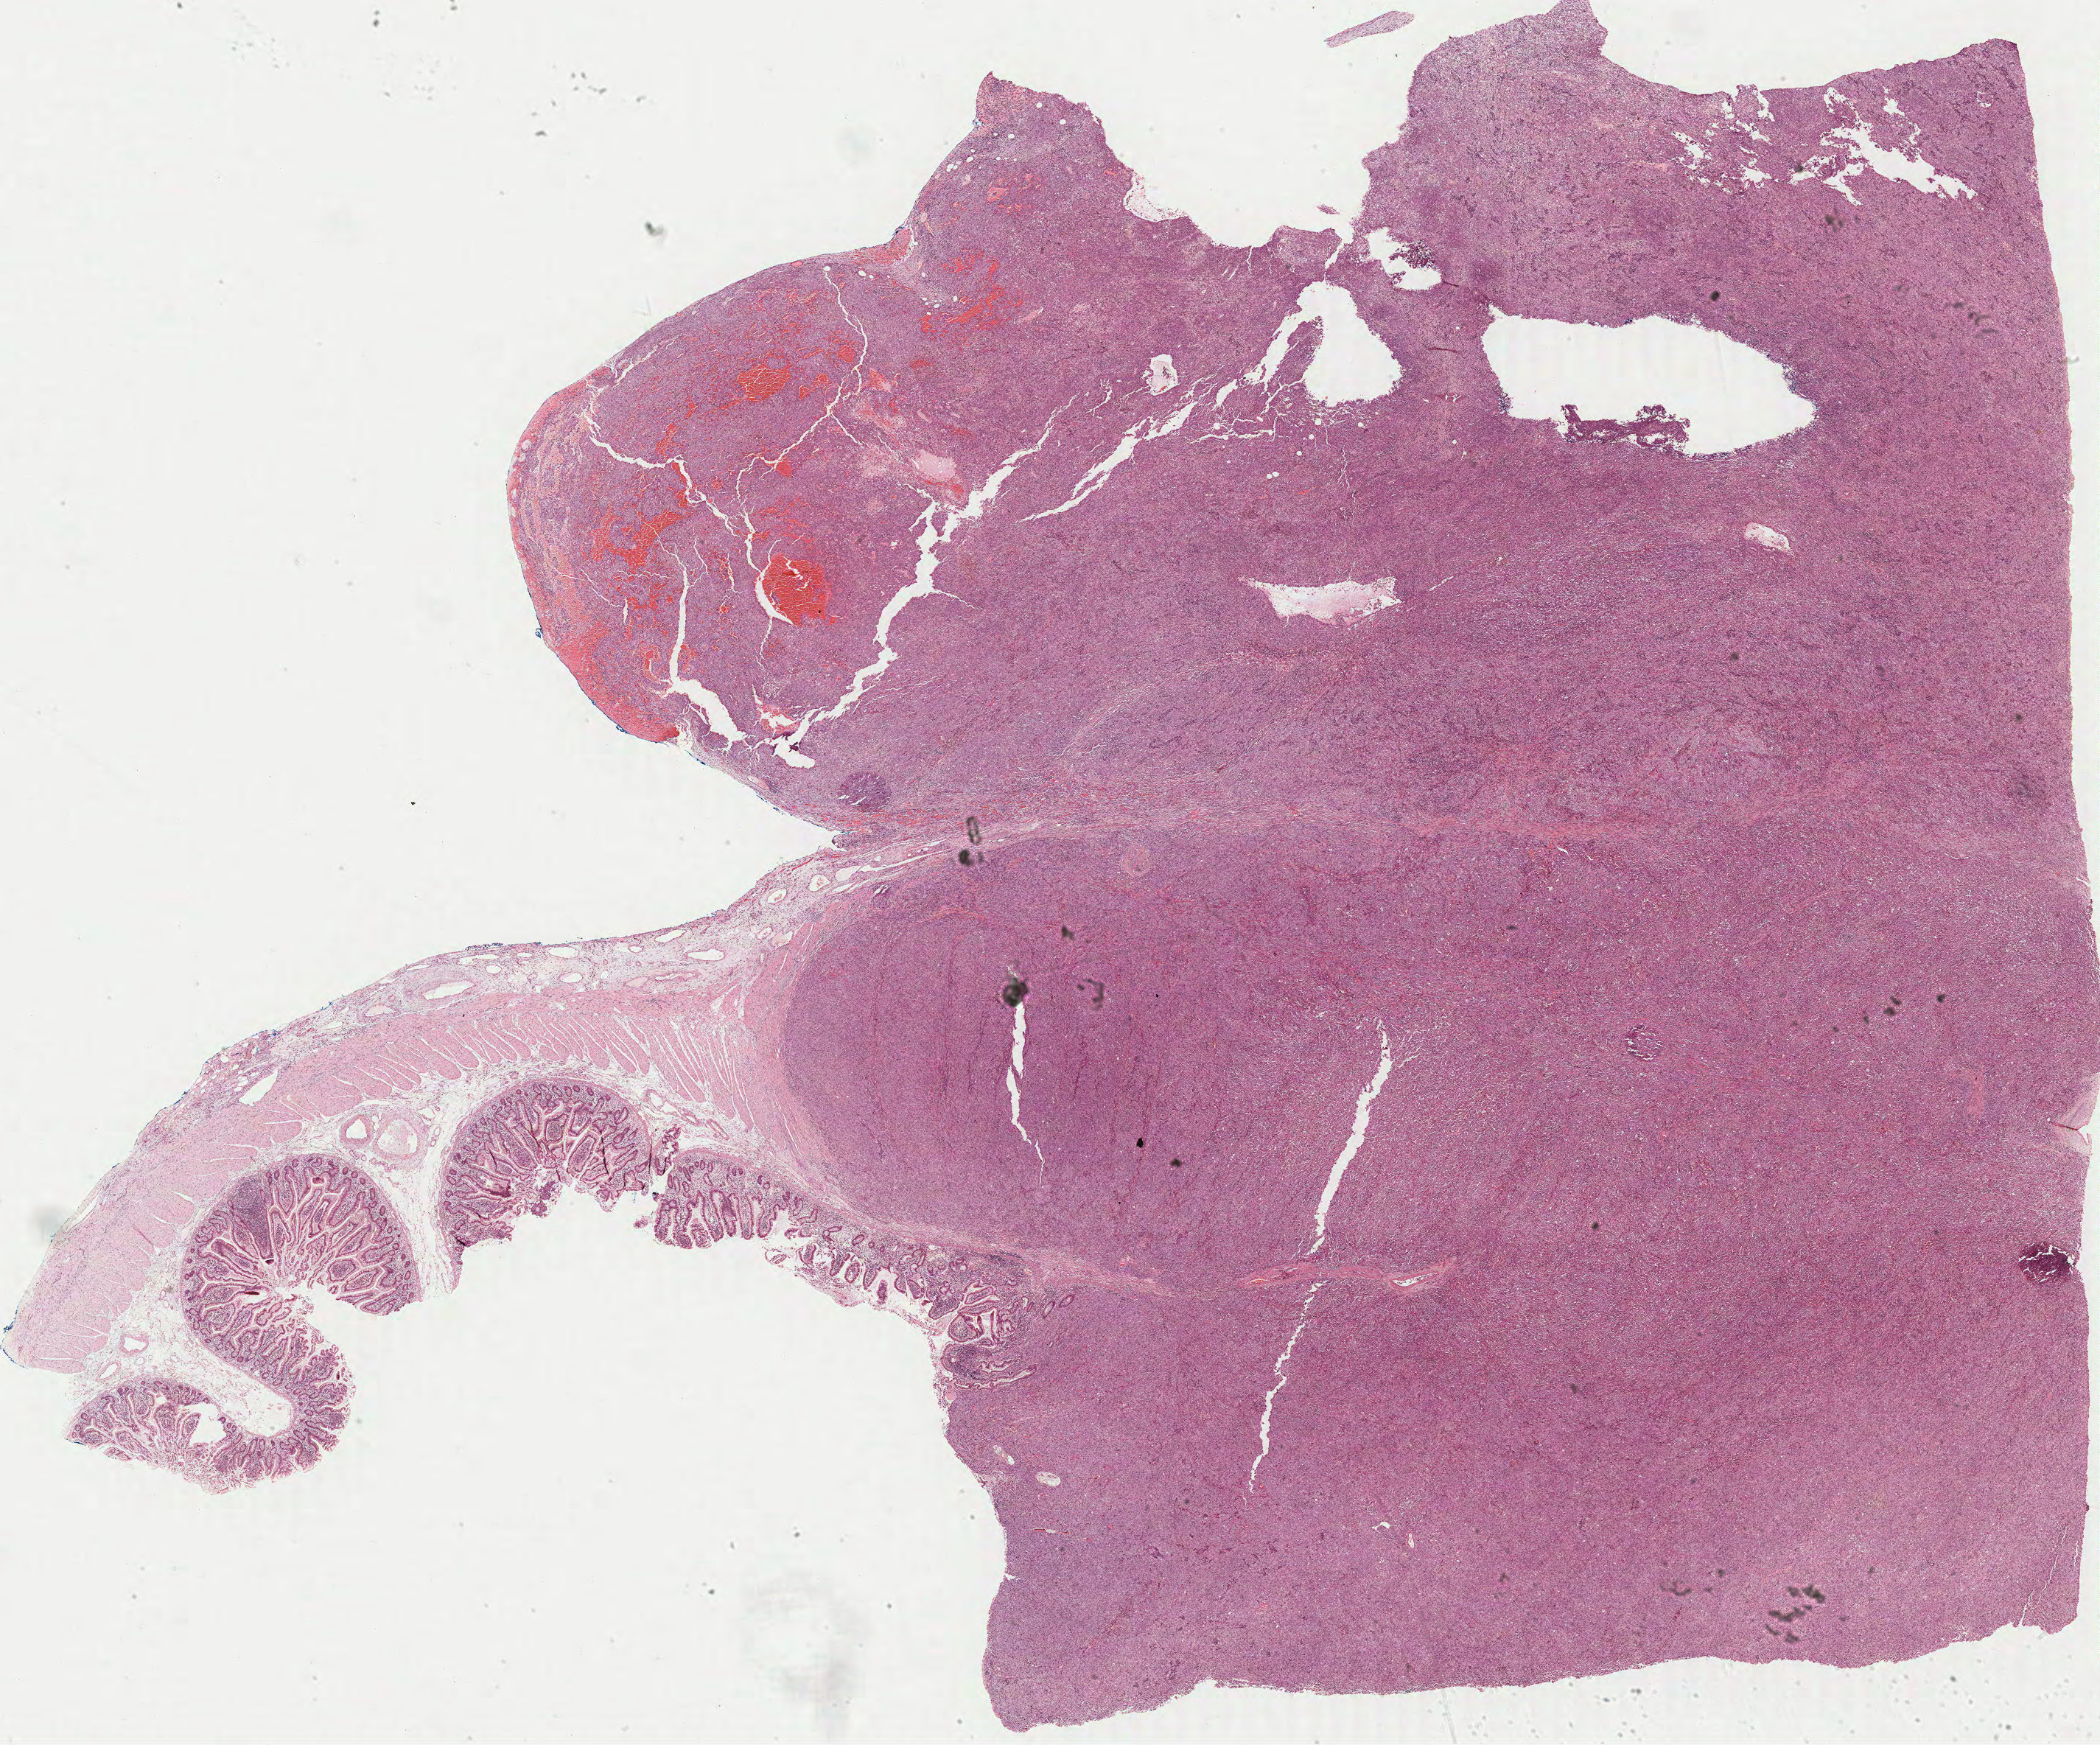
Whole-slide histology image, H&E, whole scanned area (about 22.8 x 19.0 mm) shown as a low-resolution overview; formalin-fixed paraffin-embedded (FFPE) diagnostic section; metastatic tumour sample, sampled site not recorded. Male, age 66 years at initial diagnosis.
This section: metastatic tumour tissue. Patient diagnosis: Malignant melanoma, NOS.